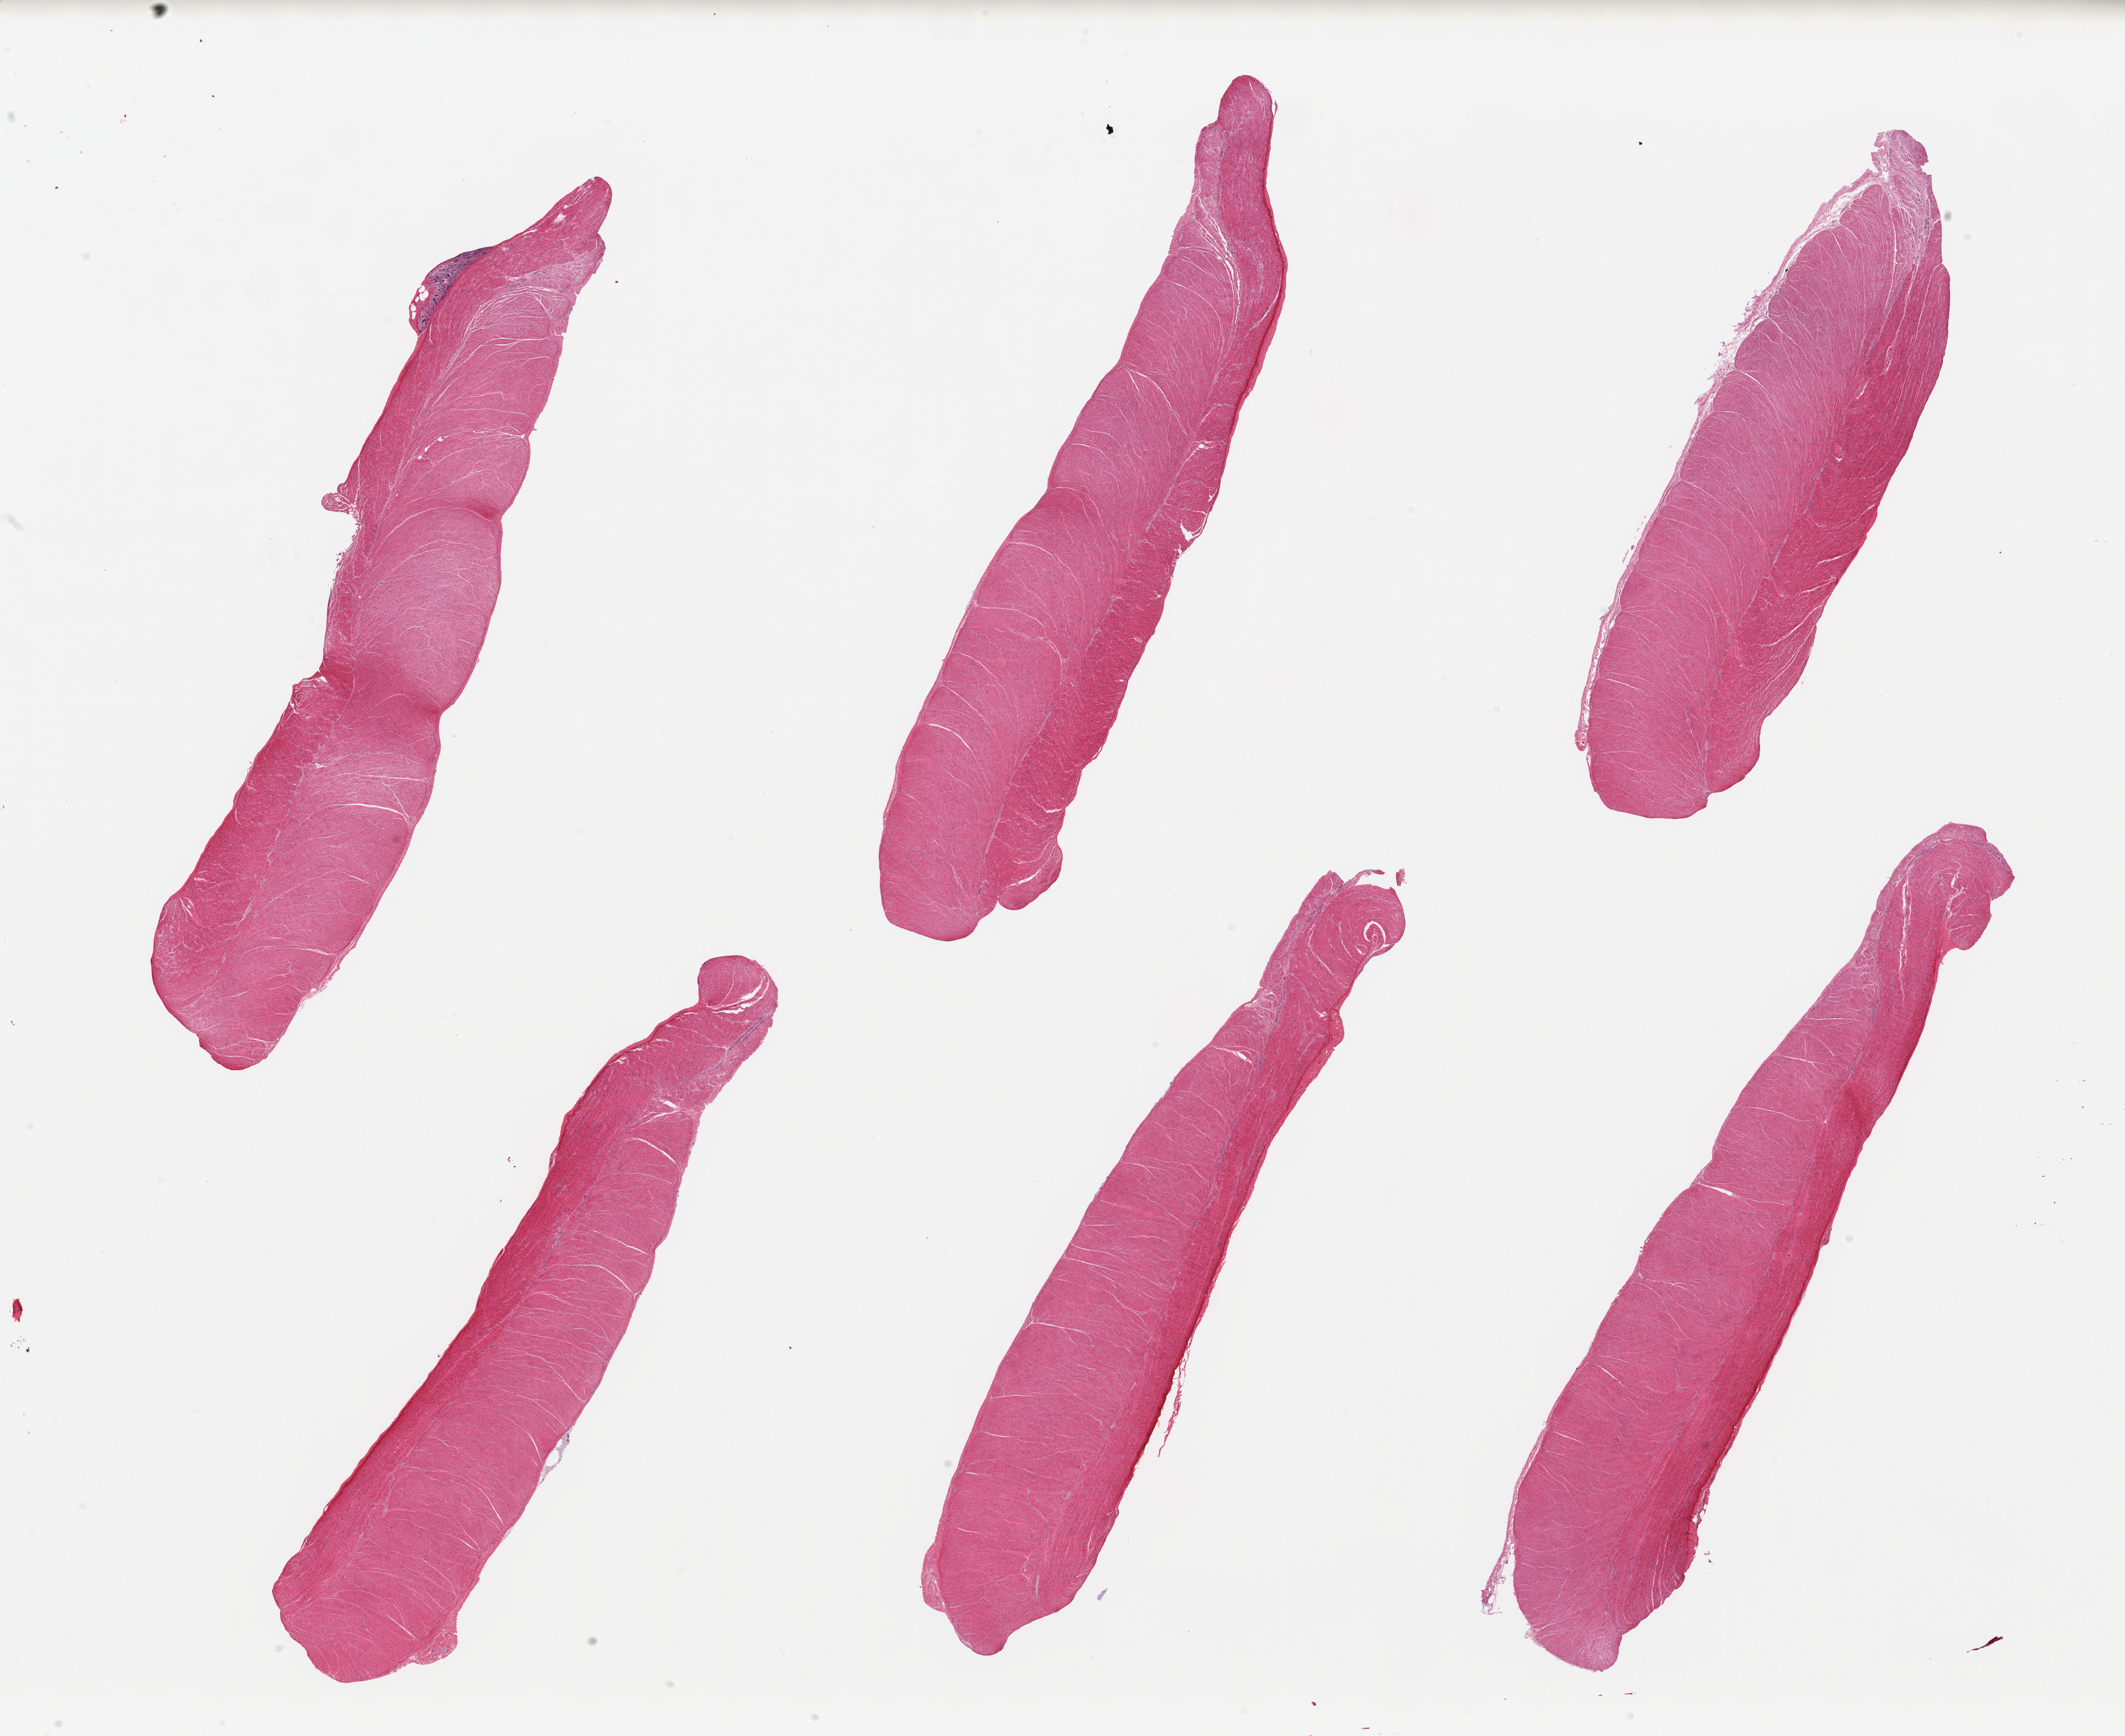
Hematoxylin and eosin (H&E) whole-slide image, brightfield, a low-resolution overview of the entire scanned area, about 28.5 x 23.3 mm; PAXgene-fixed paraffin-embedded (PFPE) section; section of sigmoid colon (target tissue); tissue donor sample. Donor: male.
Reviewer comment on this tissue sample: 6 pieces; essentially well trimmed target muscularis; attached one tiny fragment of autolyzed mucosa.